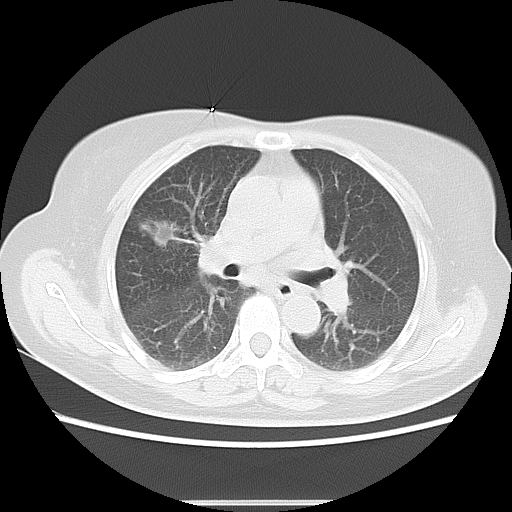
Chest CT, one axial slice. Position 6 of 17 along the scan axis. Reconstruction kernel LUNG. 120 kVp. Lung window (W 1500 / L -600 HU). 512 × 512 image matrix, field of view 350 × 350 mm. Female patient, age 57 years. From the clinical record (not read from this slice): clinical TNM (as recorded): T1c N1 M0.
Structures marked on this image (bounding box drawn by a radiologist):
- lung tumour (recorded histology: adenocarcinoma): bounding box [x1, y1, x2, y2] px = [139, 210, 177, 252]